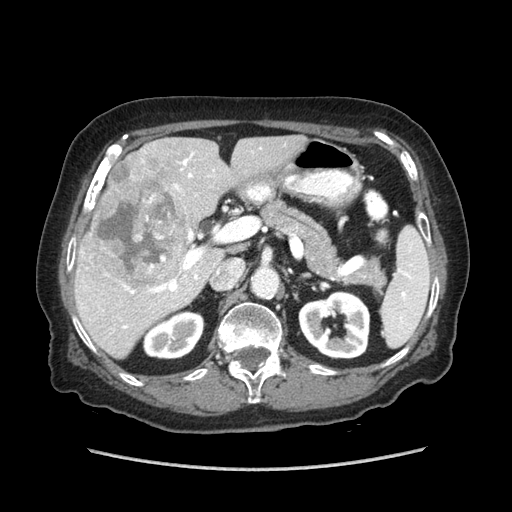
Contrast-enhanced abdominal CT (liver protocol), one axial slice; position 42 of 89 along the scan axis; reconstruction kernel STANDARD; soft-tissue window (W 400 / L 40 HU); 2.5 mm slice thickness; 512 × 512 image matrix, field of view 360 × 360 mm. From the clinical record (not read from this slice): diagnosis: hepatocellular carcinoma (patient treated with transarterial chemoembolisation; whether this scan precedes or follows treatment is not stated here); TNM stage (as recorded): Stage-IIIA; Child-Pugh class: A; tumour nodularity: multinodular; tumour size: 11 cm.
Outlined on this slice (semi-automatically segmented with operator editing):
- liver parenchyma outside the tumour (the mass and vessels are separate outlines, so this box may not span the whole liver): box from (x=74, y=134) to (x=306, y=358) px
- mass: (x=85, y=163)–(x=189, y=291)
- liver vessels: (x=122, y=152)–(x=214, y=329)